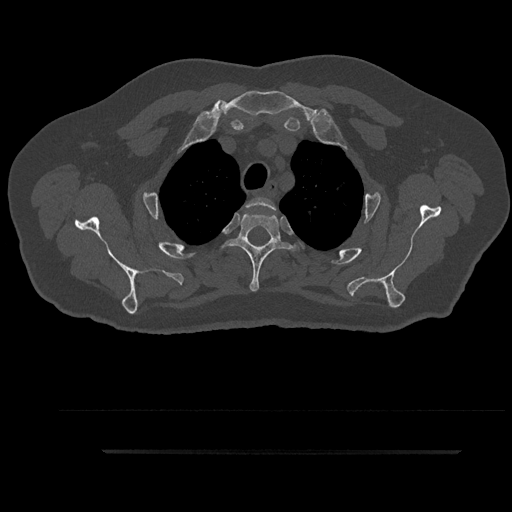
CT including the spine, one axial slice; reconstruction kernel Br40s/3; bone window (W 1800 / L 400 HU); 512 × 512 image matrix. Patient: male, 63 years. From the clinical record (not read from this slice): primary cancer: renal; vertebrae with lytic lesions (as recorded): T8.
Outlined on this slice (semi-automatic segmentation, software-assisted and operator-edited):
- T2 vertebra: bounding box (x1, y1, x2, y2) in pixels: (246, 197, 276, 211)
- T3 vertebra: (225, 212, 297, 292)